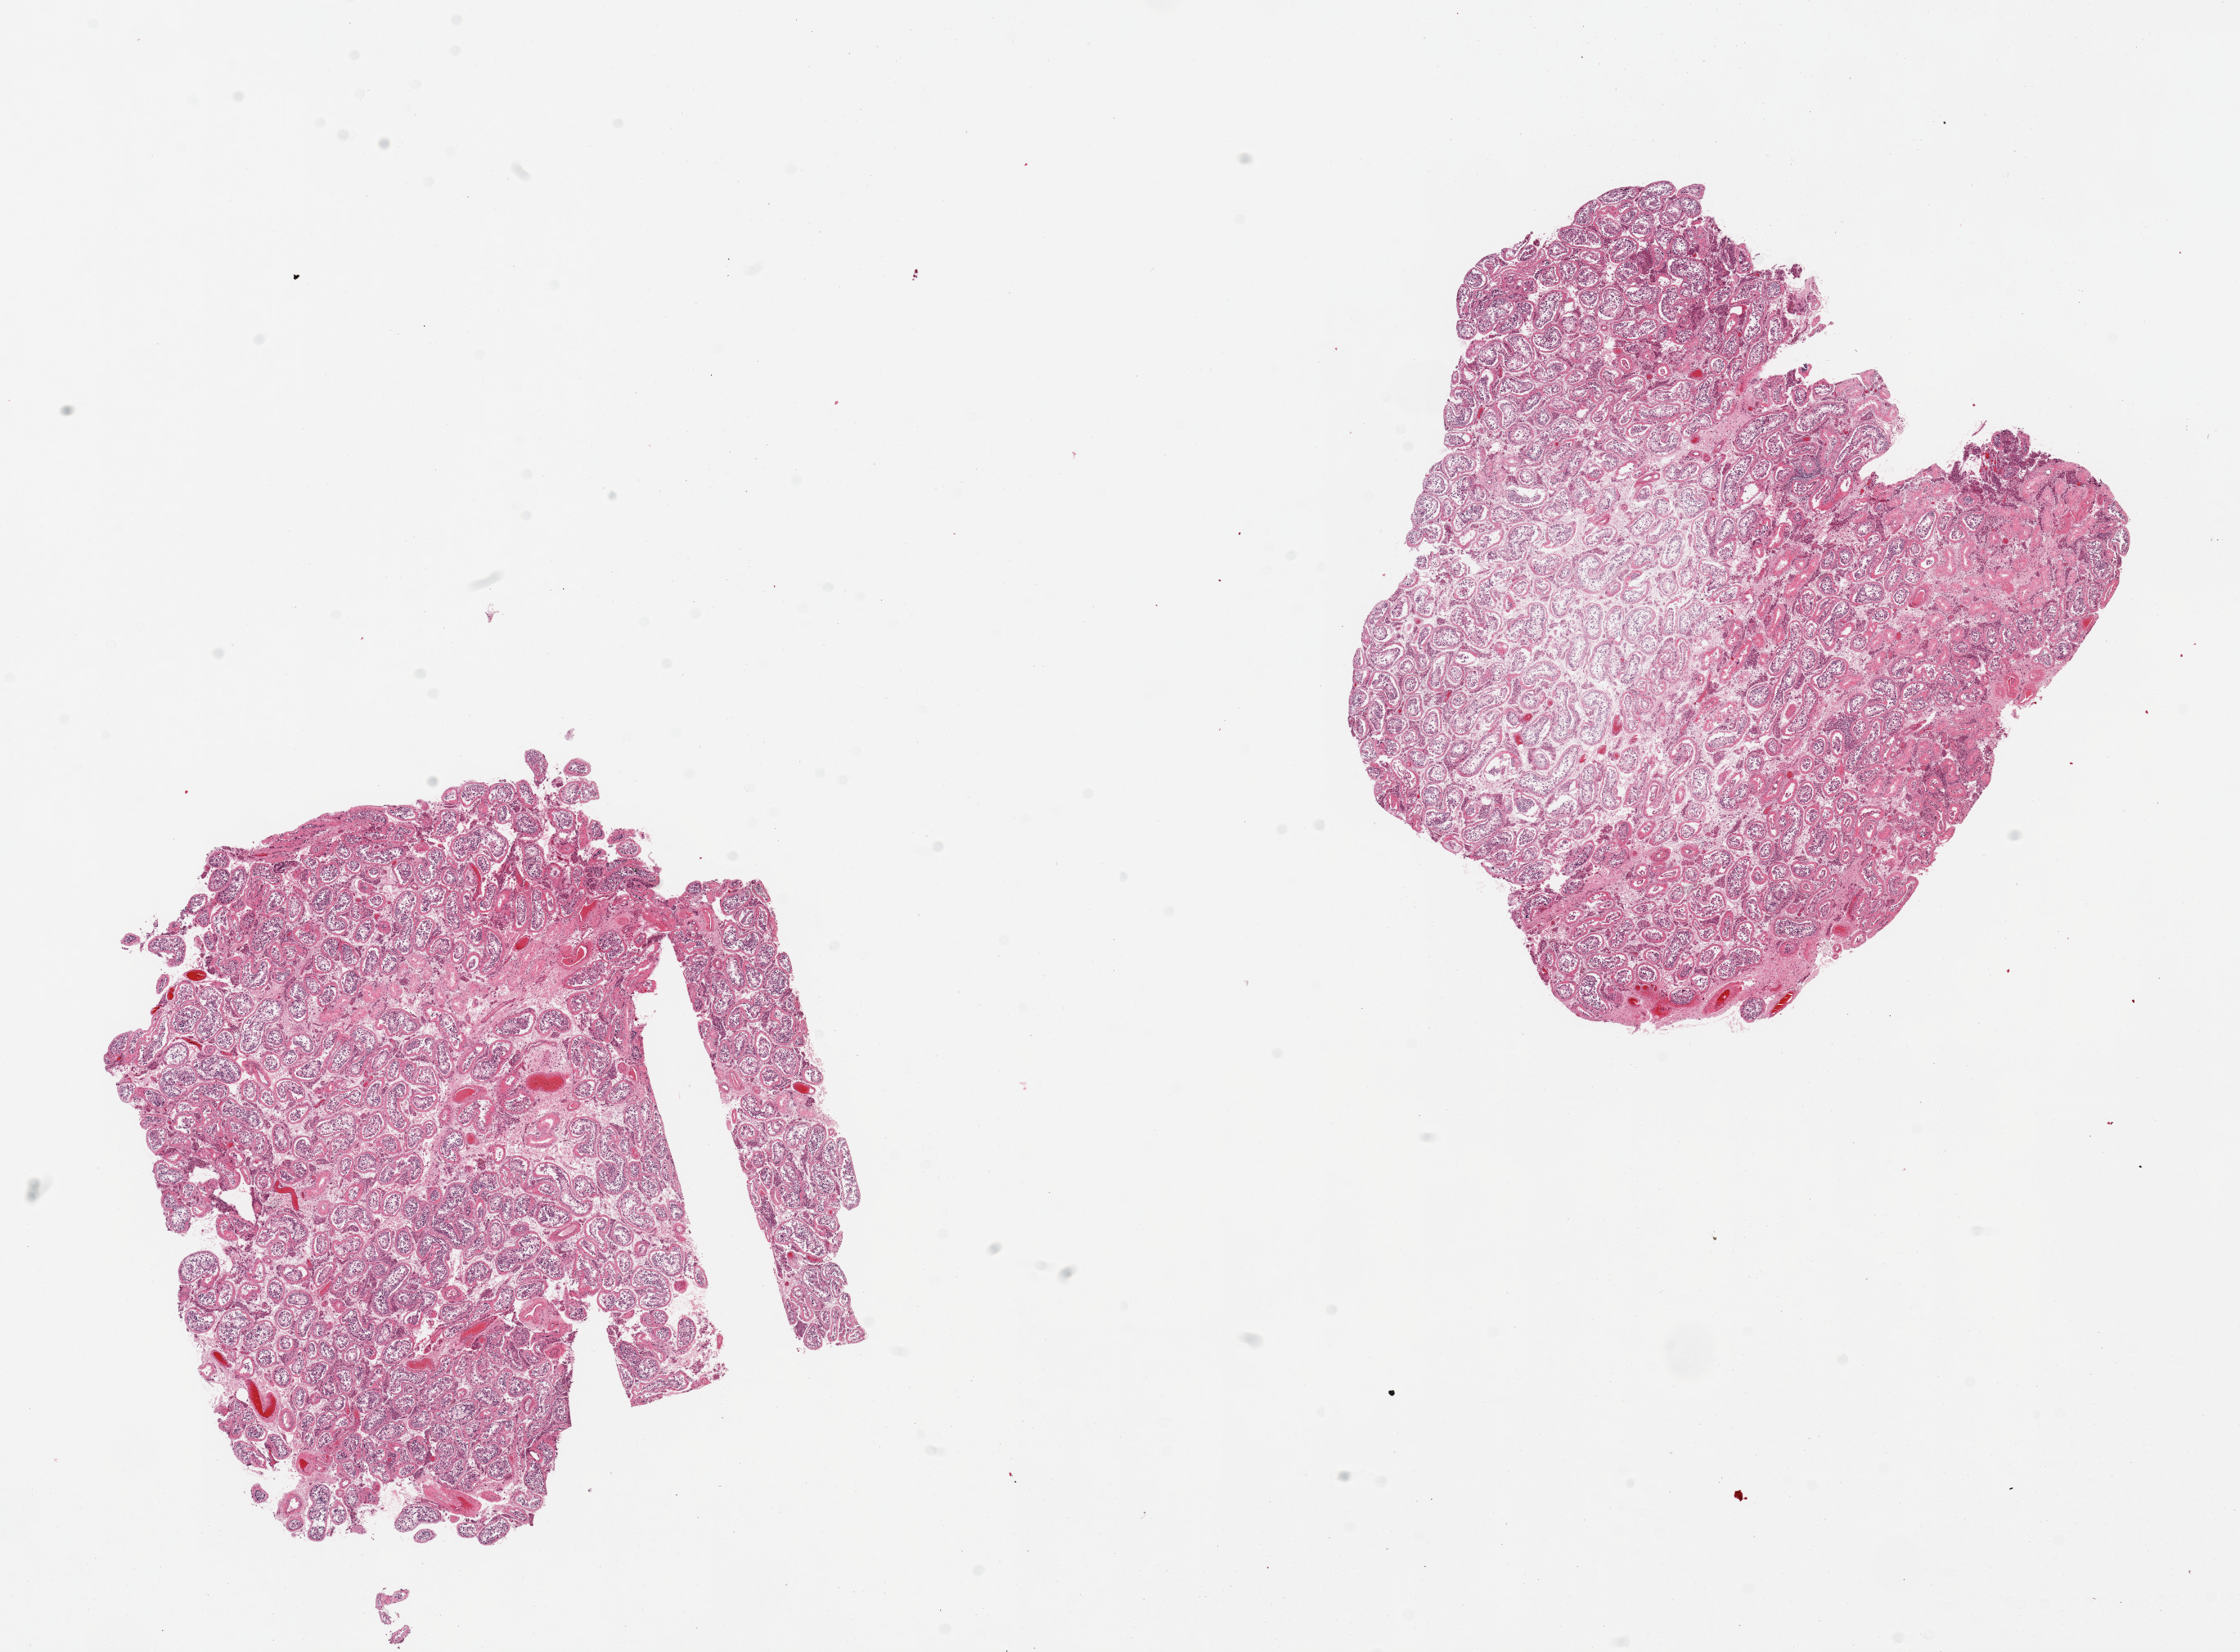
Haematoxylin and eosin whole-slide image, shown as a low-resolution overview of the whole scanned area (about 21.7 x 16.0 mm). PAXgene-fixed paraffin-embedded (PFPE) section. Target tissue: testis. Tissue donor sample.
Pathologist's review note for this sample: 2 pieces, tubules too autolyzed to assess spermatogenesis.